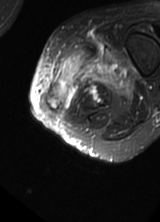
MRI of an extremity soft-tissue mass, one axial slice; position 12 of 69 along the scan axis; T2-weighted fat-saturated; MR volume resampled by the dataset authors to the PET/CT grid (not the native acquisition matrix); 3.27 mm slice thickness; 160 × 222 image matrix, field of view 156 × 217 mm. Female patient. From the clinical record (not read from this slice): histological type: pleomorphic leiomyosarcoma; grade: high; site of the primary tumour: left thigh.
Outlined on this slice (expert contour drawn on MRI and transferred to this co-registered scan by the dataset authors):
- gross tumour volume including surrounding oedema: box from (x=48, y=40) to (x=133, y=112) px